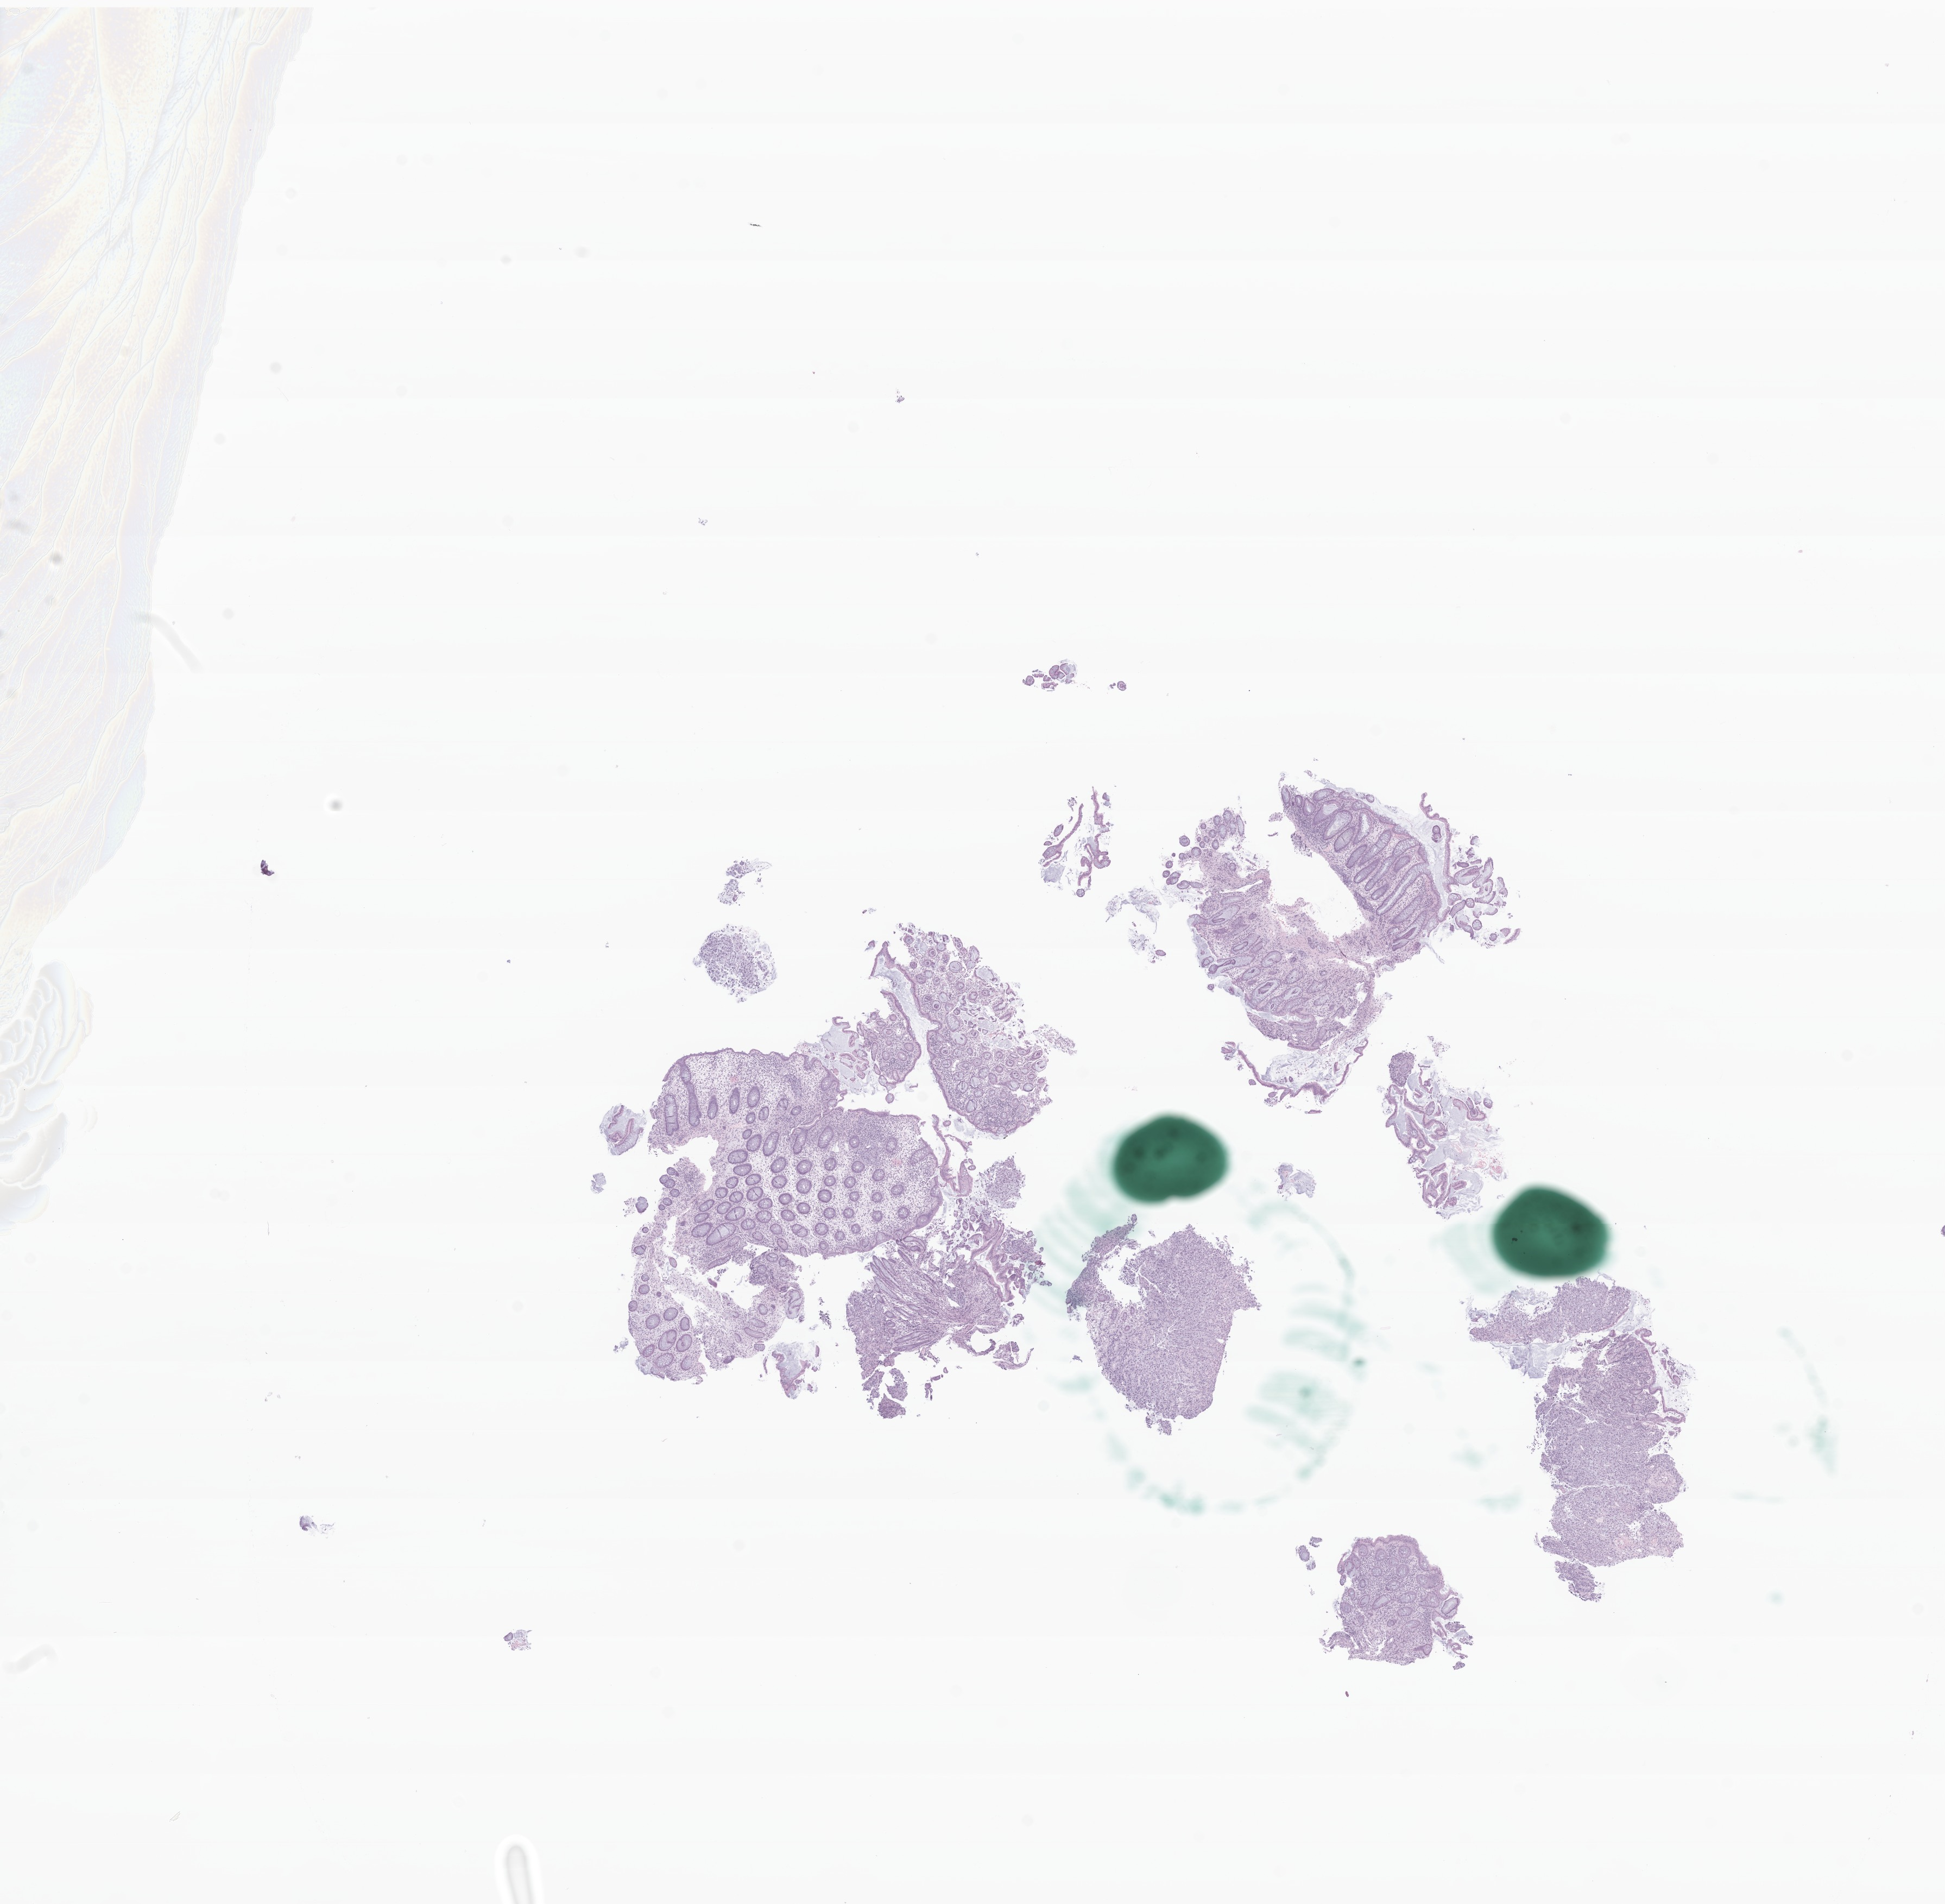
Whole-slide image, hematoxylin and eosin (H&E) stain of tumor tissue from the rectosigmoid junction — a low-resolution overview of the entire scanned area, about 15.1 x 14.7 mm, FFPE section. Male patient, age 151 months (12 years 7 months).
• diagnosis (ICD-O-3 morphology term): Metastatic signet ring cell carcinoma